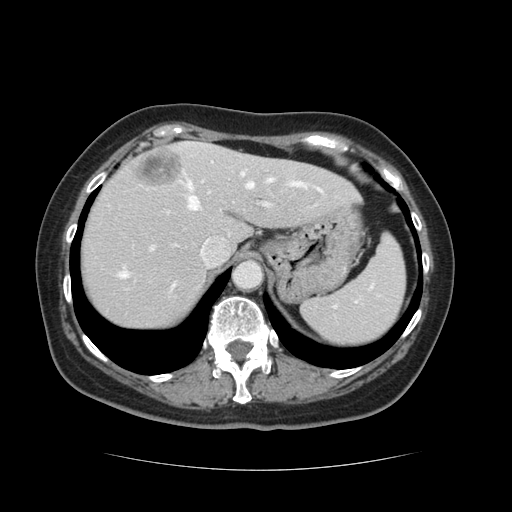
Contrast-enhanced abdominal CT, one axial slice; slice 97 of 128 in the series (ordered by position); 120 kVp; soft-tissue window (W 400 / L 40 HU); 512 × 512 image matrix, field of view 366 × 366 mm. Female patient, age 67 years. From the clinical record (not read from this slice): diagnosis: colorectal cancer liver metastases, imaged before liver resection; multiple liver metastases: yes; largest metastasis: 3 cm; disease in both lobes: yes.
Annotated regions visible in this slice (expert manual segmentation):
- hepatic veins: bounding box [x1, y1, x2, y2] px = [119, 172, 320, 293]
- liver: [80, 143, 358, 330]
- planned liver remnant (the part of the liver to remain after resection): [80, 153, 358, 330]
- portal vein (with intrahepatic branches): [152, 160, 272, 249]
- liver metastasis: [134, 150, 180, 187]